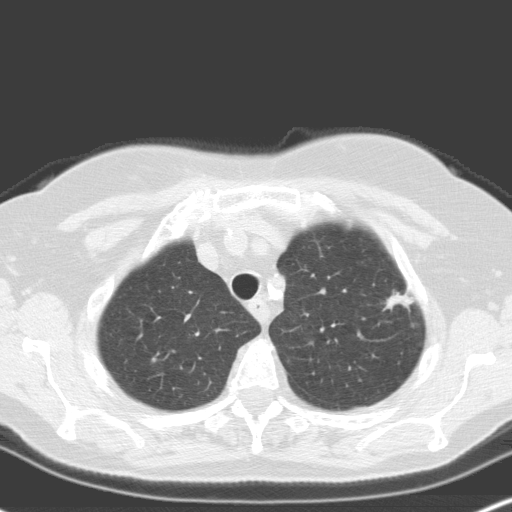
Low-dose screening chest CT, one axial slice. Position 138 of 160 along the scan axis. Lung window (W 1500 / L -600 HU). 512 × 512 image matrix.
Structures marked on this image (outlined manually by an expert reader):
- lesion 2 (nodule): bounding box <385,292,414,309> (left, top, right, bottom; pixels)